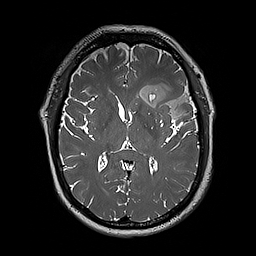
Brain MRI from a brain-tumour surgery series, one axial slice; slice 107 of 192 in the series (ordered by position); 256 × 256 image matrix, field of view 250 × 250 mm. Case-level facts recorded for this patient, not image findings: histopathology: Oligodendroglioma; WHO grade: 3; IDH mutation: yes; tumour location: Left Sylvian Fissure (Temporal).
Structures marked on this image (manually delineated by an expert):
- tumour: box from (x=124, y=80) to (x=197, y=120) px